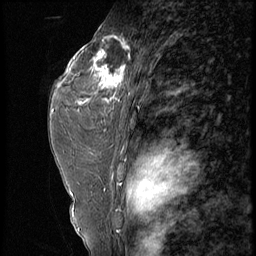
Breast MRI (dynamic contrast-enhanced), one sagittal slice; position 36 of 56 along the scan axis; 4 images stored at this slice position (order not interpretable as contrast timing); 1.5 T; TE 4.2 ms, TR 9 ms; 2.5 mm slice thickness; 256 × 256 image matrix, field of view 180 × 180 mm. Patient: female, 44 years. Case-level facts recorded for this patient, not image findings: setting: breast cancer imaged before/during neoadjuvant chemotherapy; receptor status: triple-negative.
Annotated regions visible in this slice (semi-automatically segmented with operator editing):
- analysis volume of interest (the breast-tissue region the enhancement analysis was run in; not a lesion): box from (x=87, y=28) to (x=132, y=99) px
- tumour enhancement mask (voxels above the 140 % enhancement threshold inside the analysis volume of interest): (x=87, y=35)–(x=130, y=99)